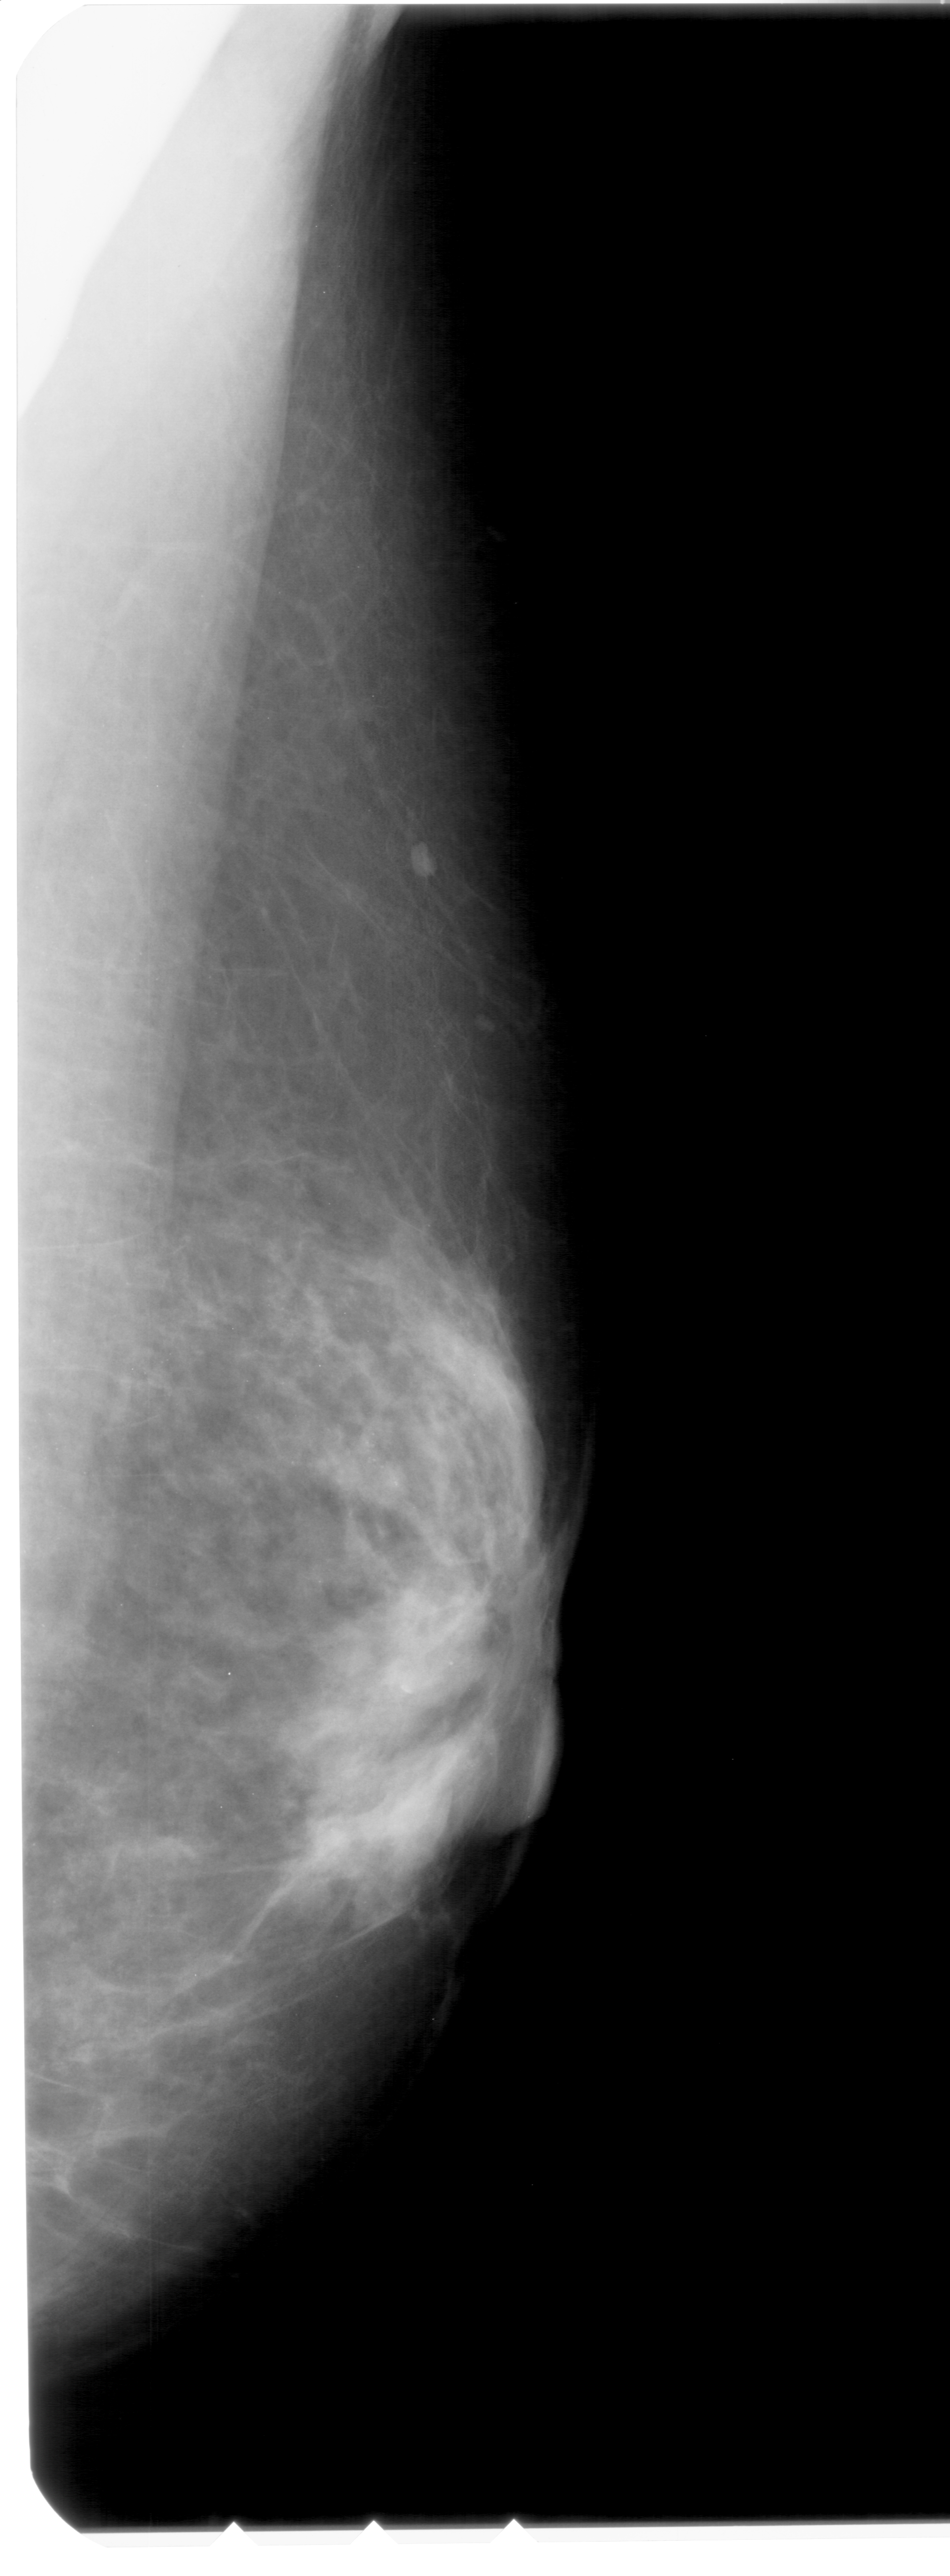
Scanned film-screen mammogram, right breast, mediolateral oblique (MLO) view, breast composition: heterogeneously dense (BI-RADS density category 3 of 4).
Calcifications, morphology pleomorphic, distribution clustered; BI-RADS assessment category 4; pathology result (as recorded, not read from the image): malignant.